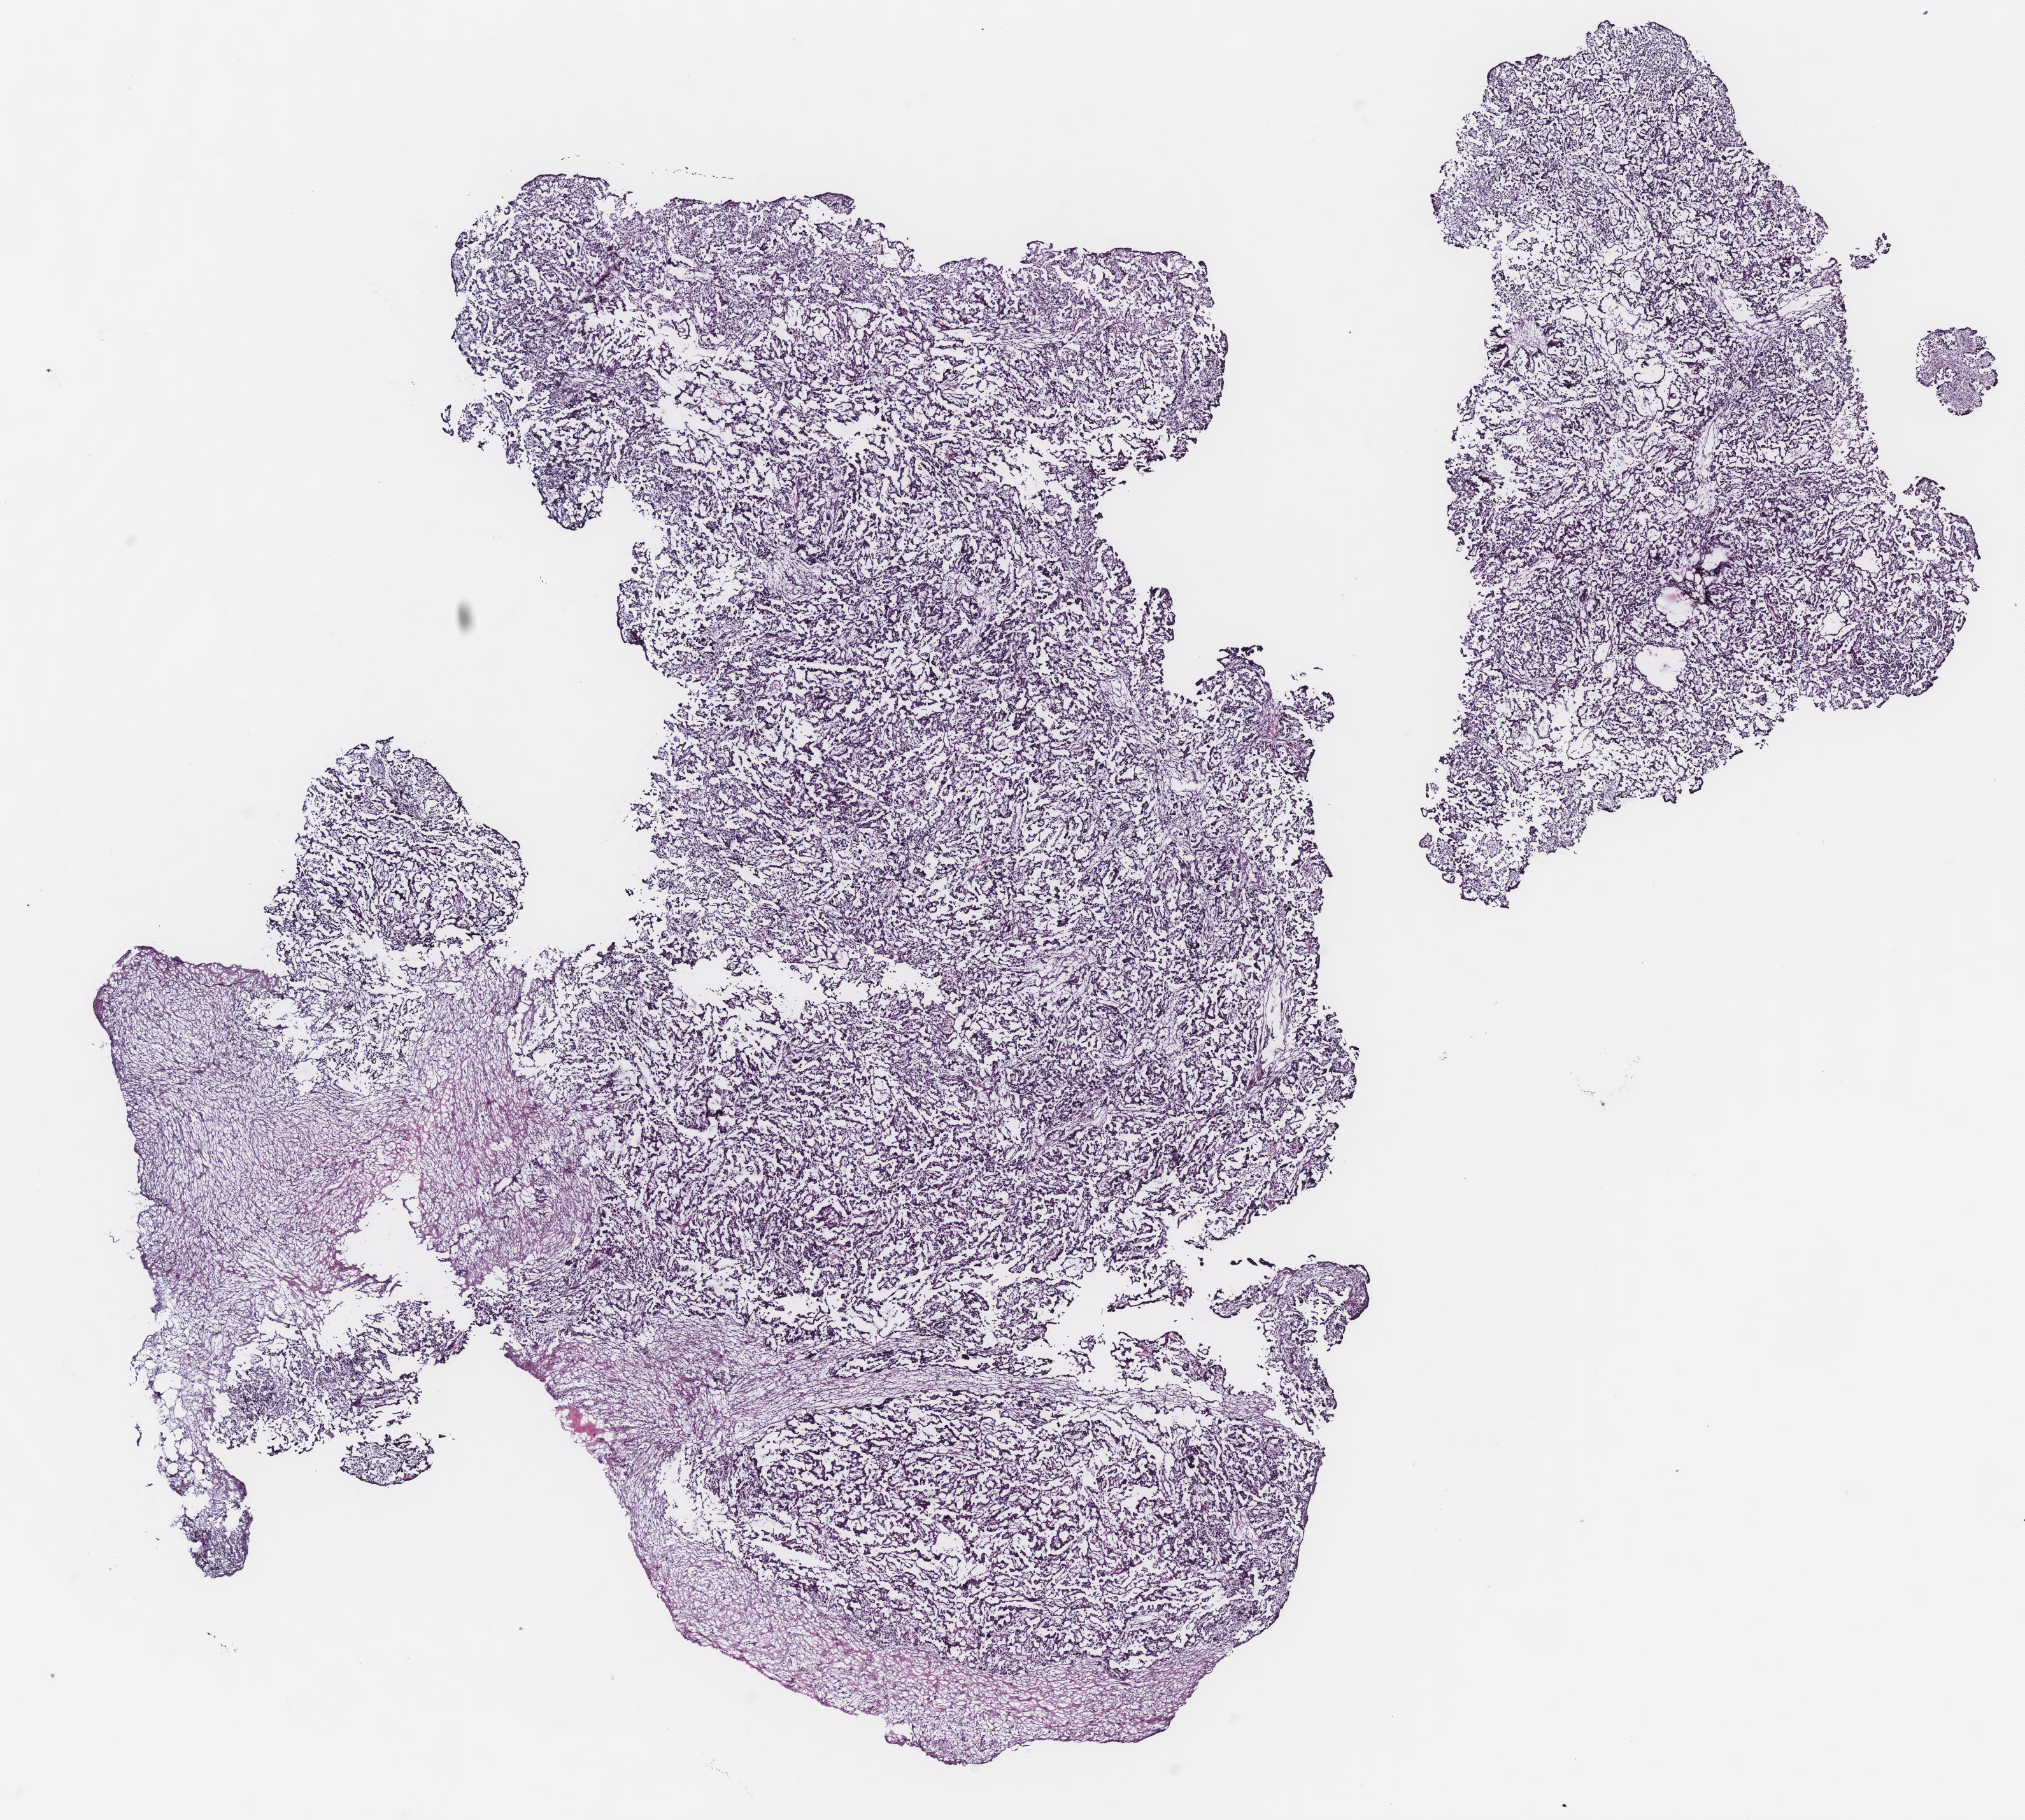
Whole-slide histology image, H&E — whole scanned area (about 12.7 x 11.4 mm) shown as a low-resolution overview; ovary, tissue type not recorded. Patient sex: female.
Patient diagnosis: Serous adenocarcinoma, NOS.